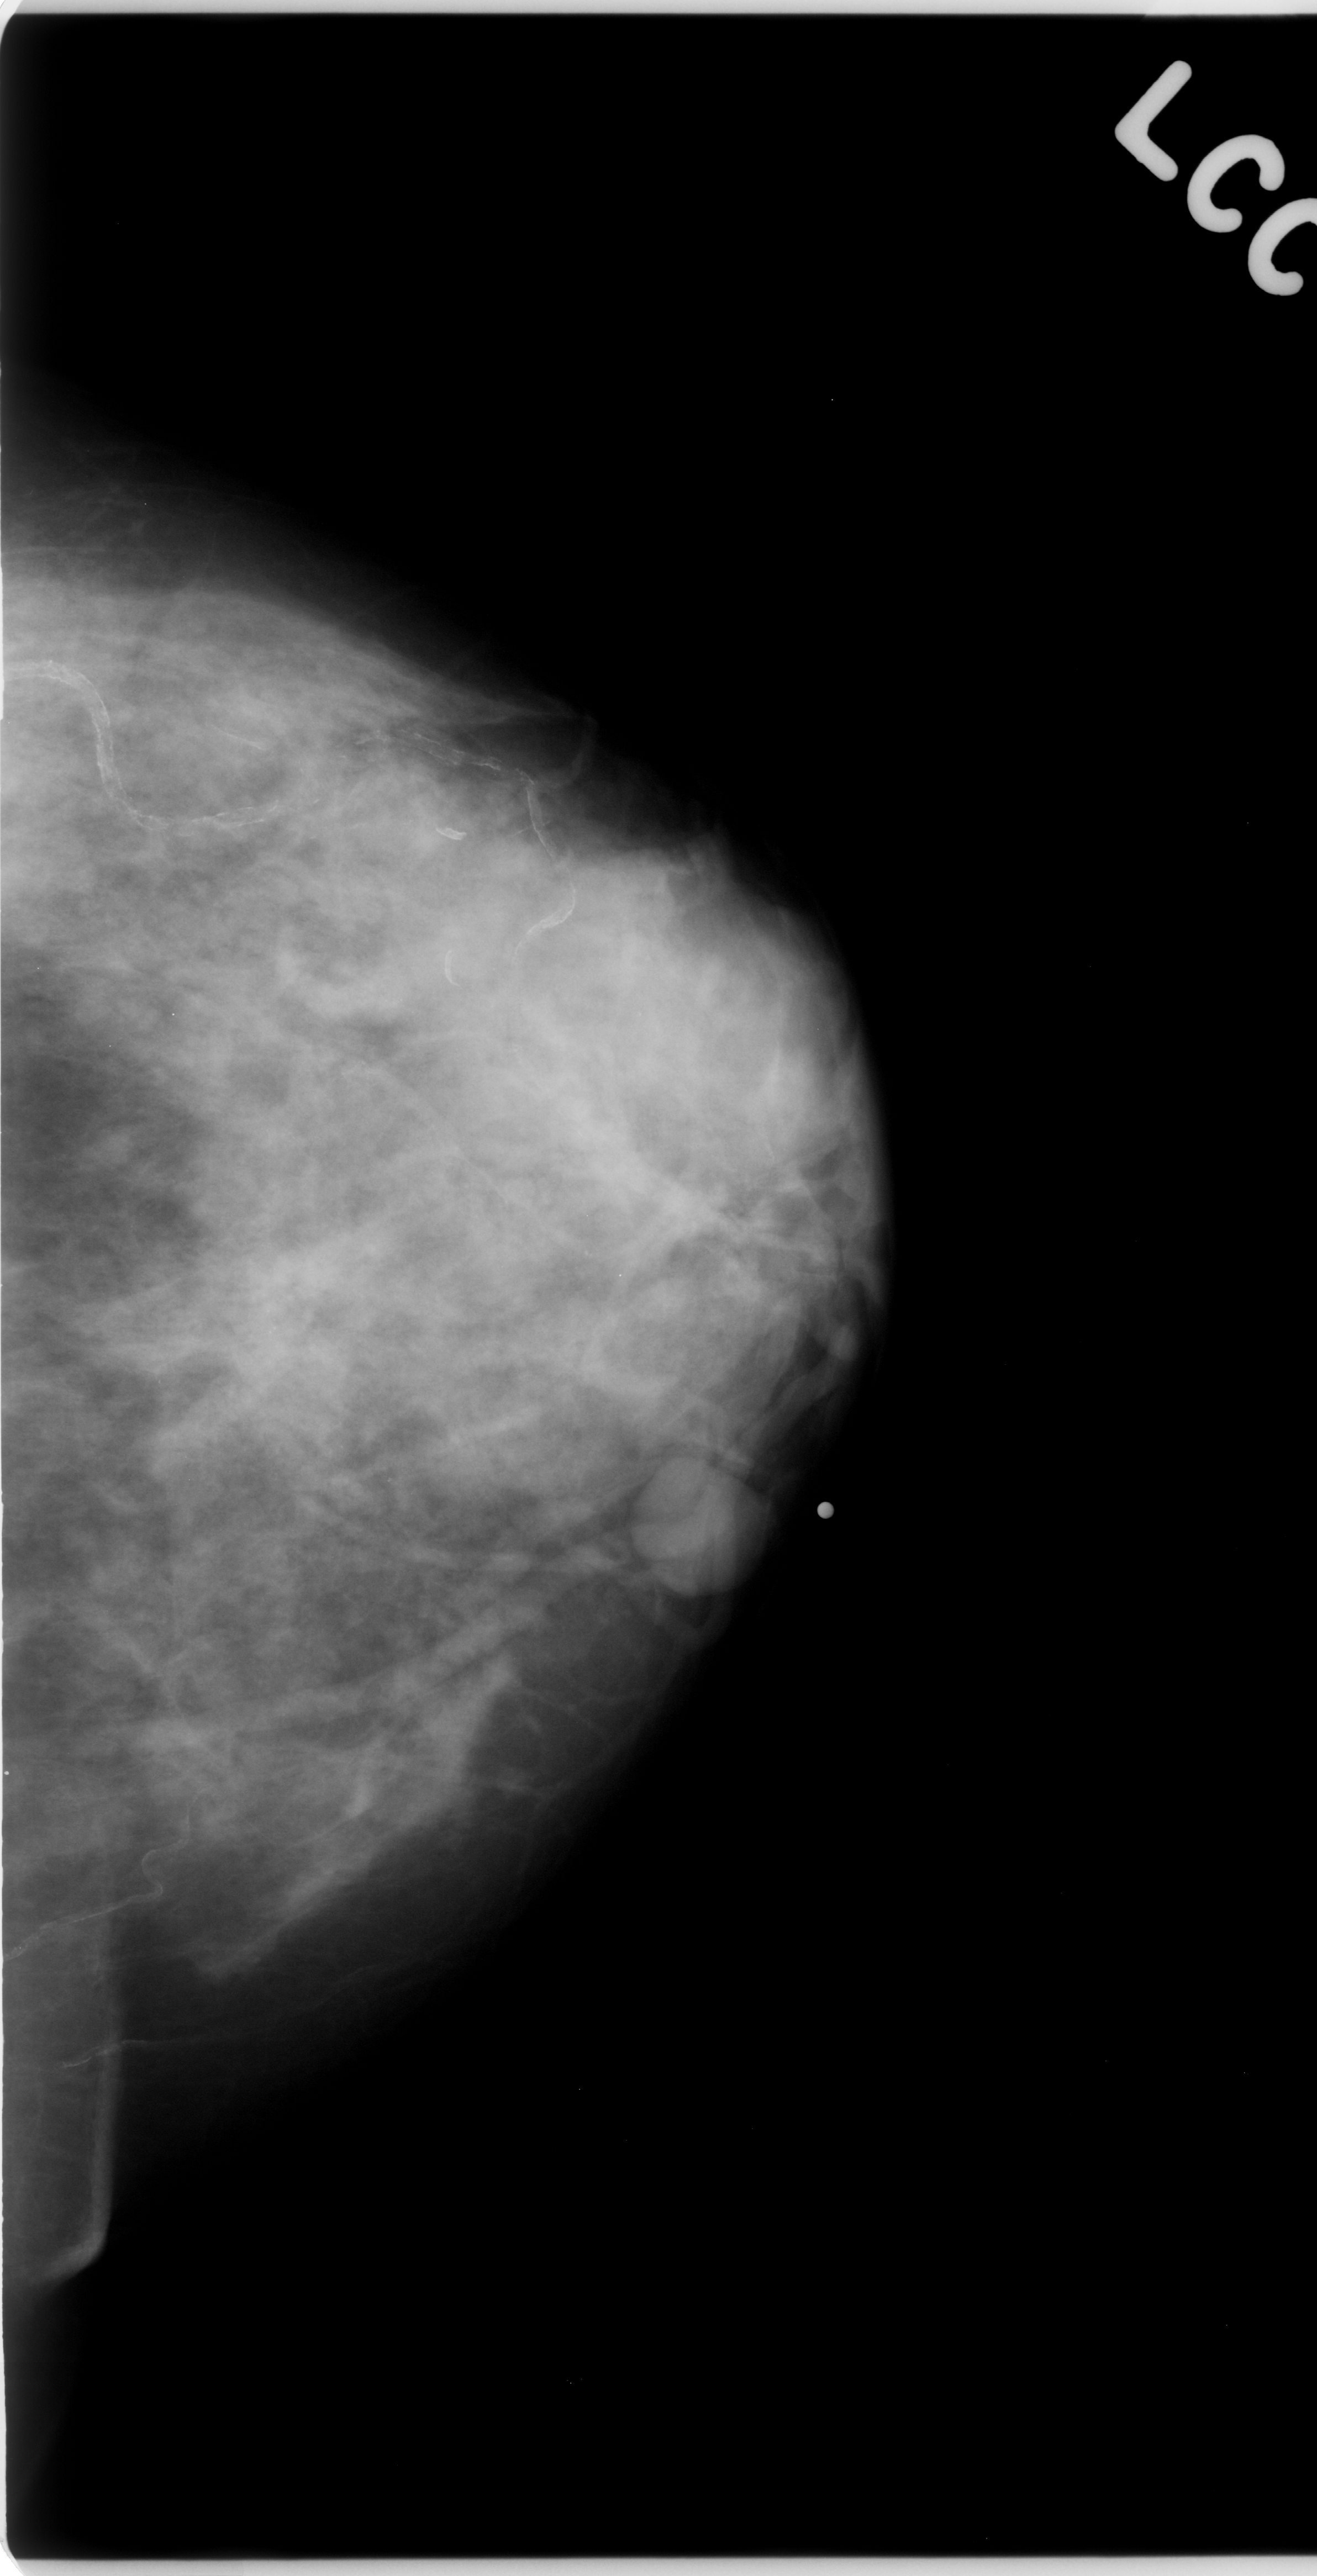
Digitized screen-film mammogram, left breast, craniocaudal (CC) view, breast composition: heterogeneously dense (BI-RADS density category 3 of 4).
Abnormality record for this image: mass, shape oval, margins circumscribed; BI-RADS assessment category 3; pathology (as recorded): benign.